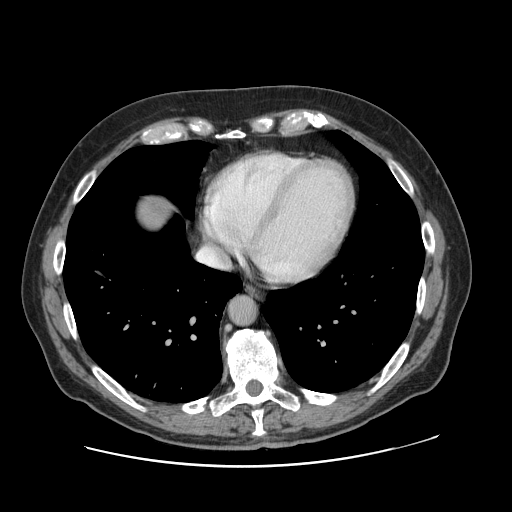
Contrast-enhanced abdominal CT, one axial slice. Slice 120 of 138 in the series (ordered by position). Intravenous contrast given. Soft-tissue window (W 400 / L 40 HU). 2.5 mm slice thickness. 512 × 512 image matrix. Male patient, age 71 years. From the clinical record (not read from this slice): diagnosis: colorectal cancer liver metastases, imaged before liver resection; multiple liver metastases: no; largest metastasis: 3.3 cm; disease in both lobes: no.
Outlined on this slice (outlined manually by an expert reader):
- liver: box from (x=132, y=194) to (x=178, y=231) px
- planned liver remnant (the part of the liver to remain after resection): (x=134, y=193)–(x=177, y=231)